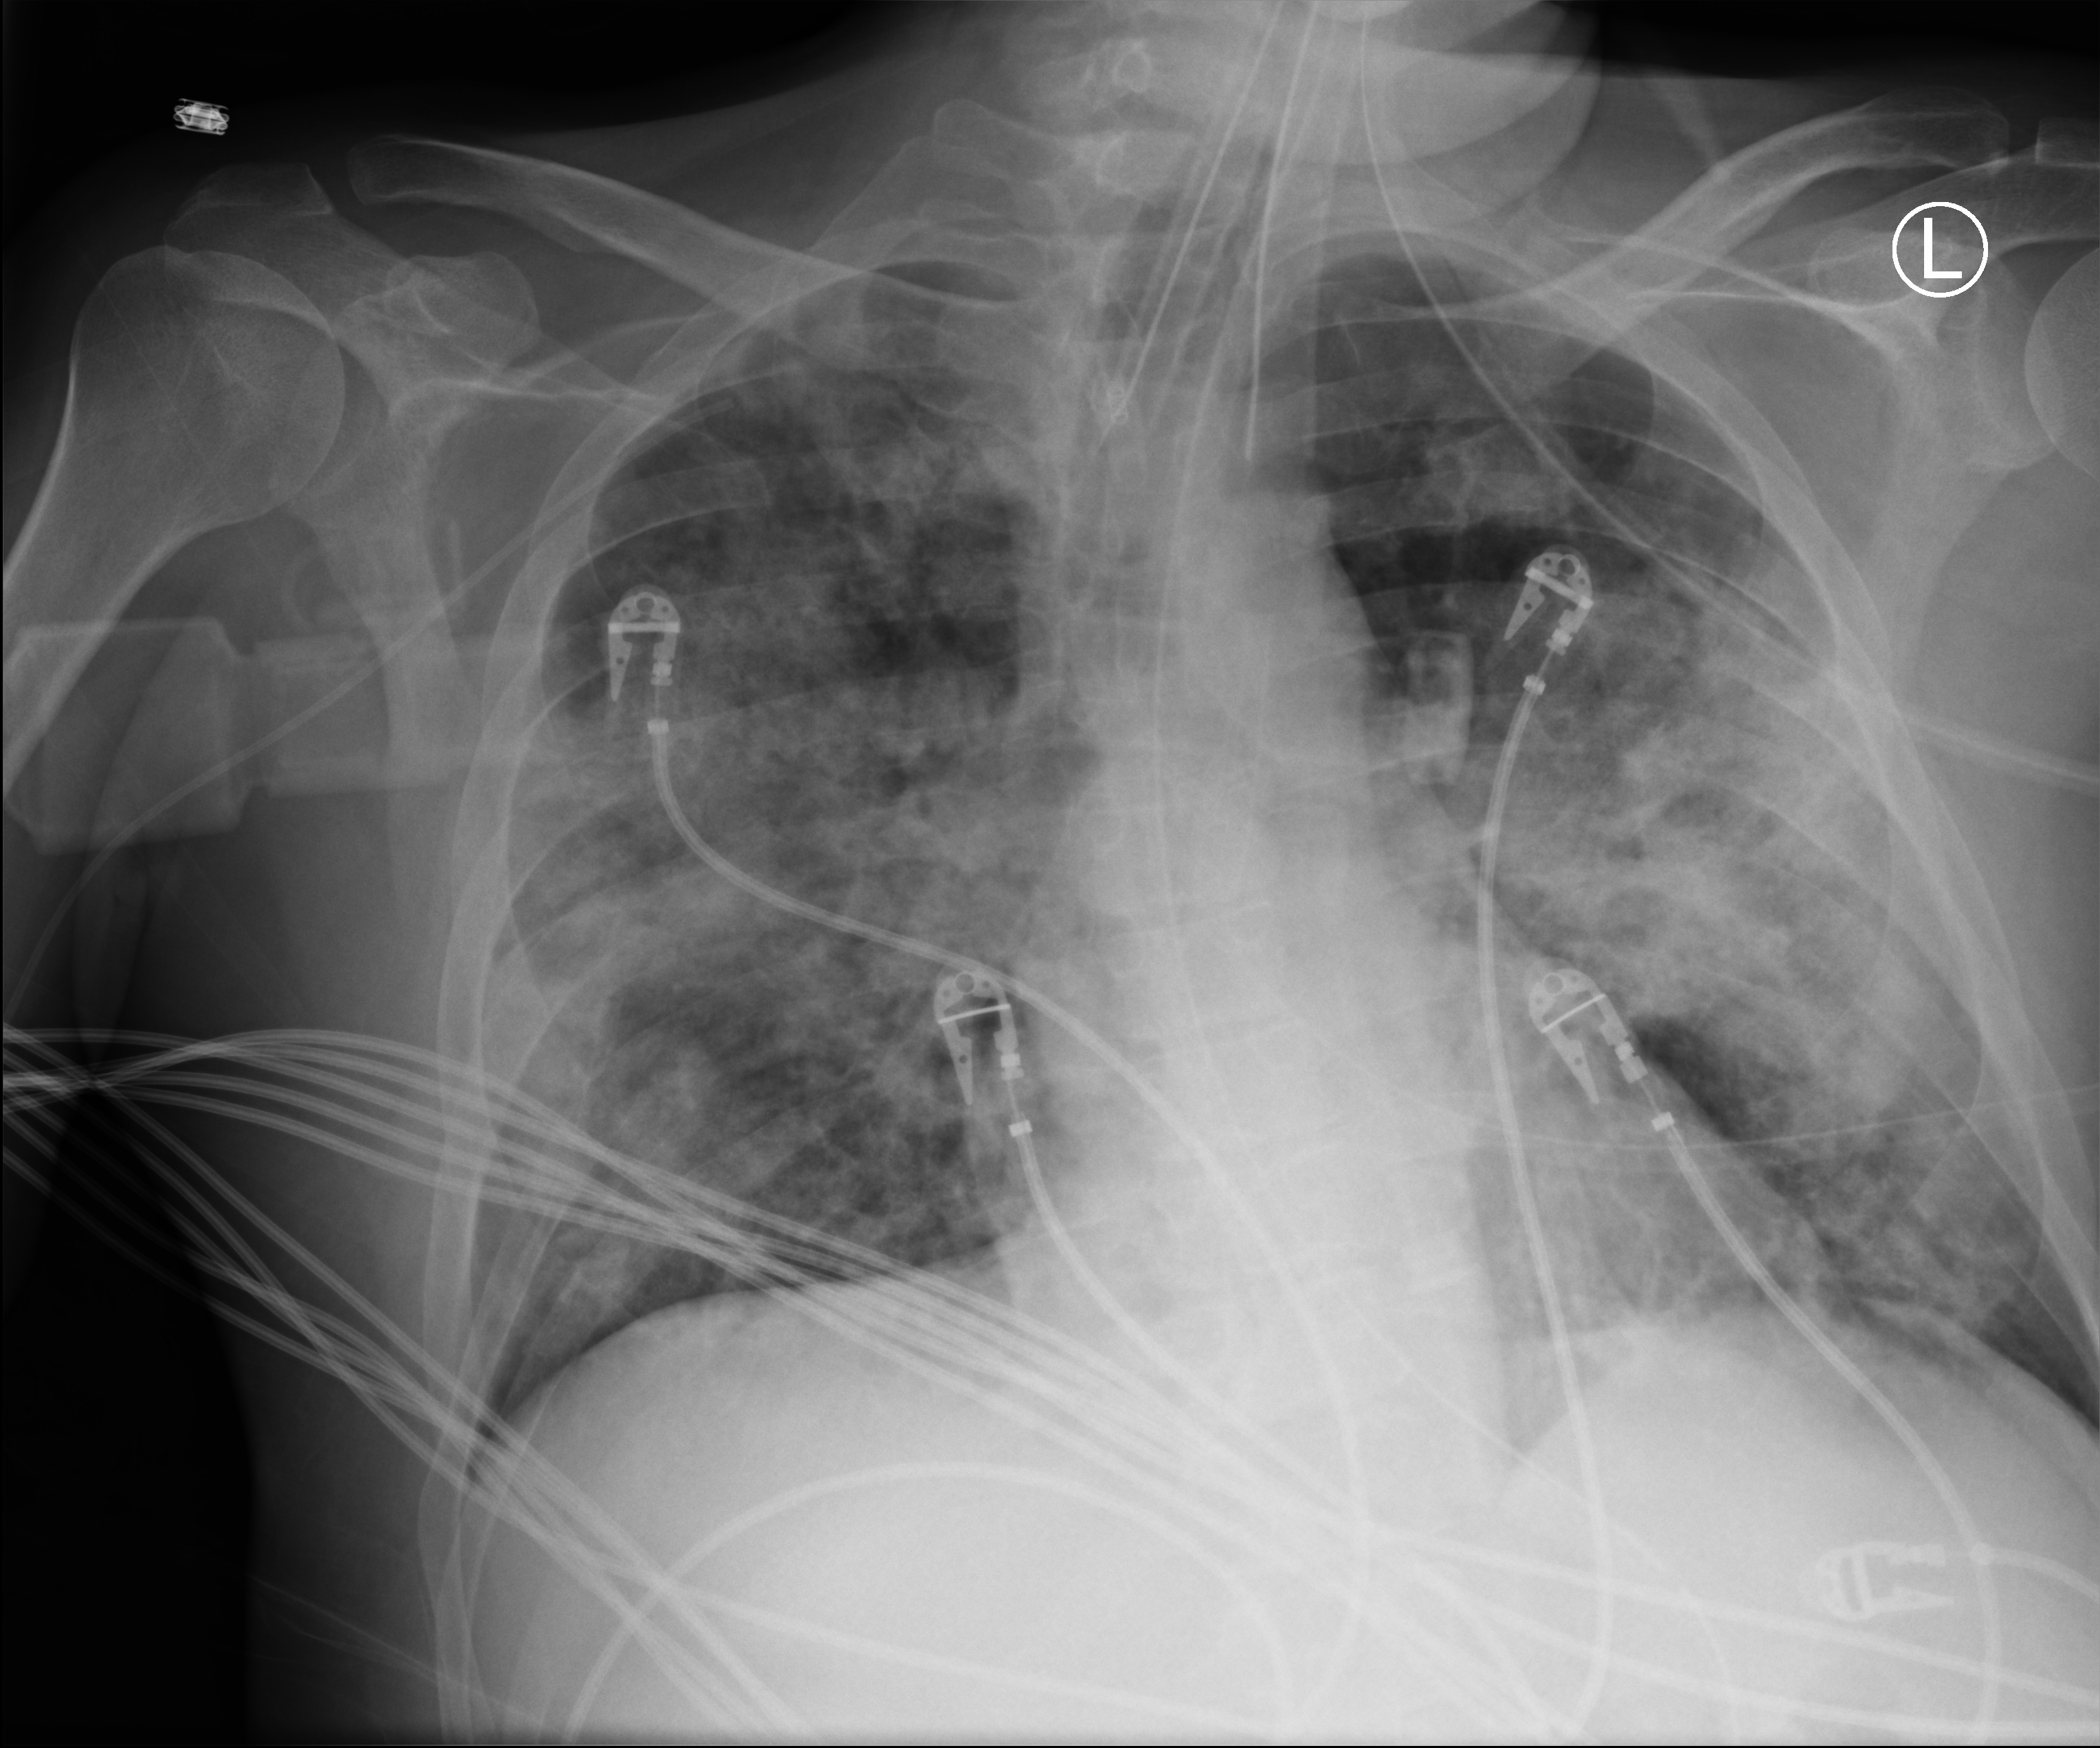
Portable chest radiograph. Male patient hospitalised with COVID-19, age 18–59 years.
Hospital-stay facts (about this admission, not read from this image; timing relative to this image not recorded):
- admitted to intensive care during this hospital stay: yes
- length of hospital stay: 20 days